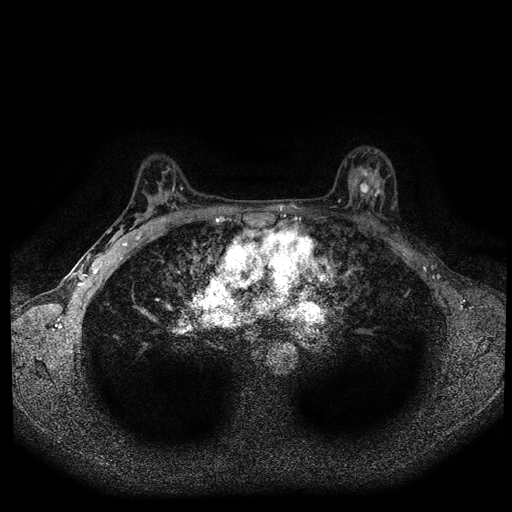
Breast MRI (dynamic contrast-enhanced, multi-phase), one axial slice. Slice 61 of 108 in the series (ordered by position). Dynamic contrast-enhanced series, time point 2 of 5 at this slice position (early post-contrast). 1.5 T. TE 2.7 ms, TR 5.5 ms. 2 mm slice thickness. 512 × 512 image matrix, field of view 320 × 320 mm. Patient: female, 36 years.
Structures marked on this image (semi-automatically segmented with operator editing):
- breast lesion (labelled 'tumour' in the annotation; benign lesions carry a separate 'benign' label): bounding box [x1, y1, x2, y2] px = [348, 164, 386, 203]